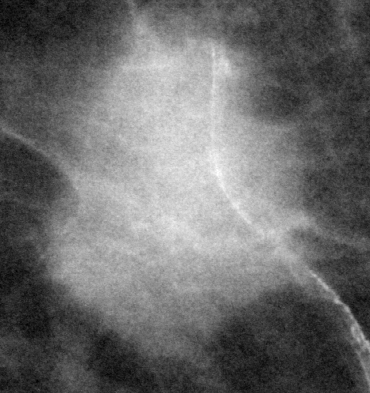
Crop from a digitized film mammogram around one marked abnormality, right breast, CC view.
Mass, shape irregular, margins spiculated; BI-RADS assessment category 5; pathology result (as recorded, not read from the image): malignant.